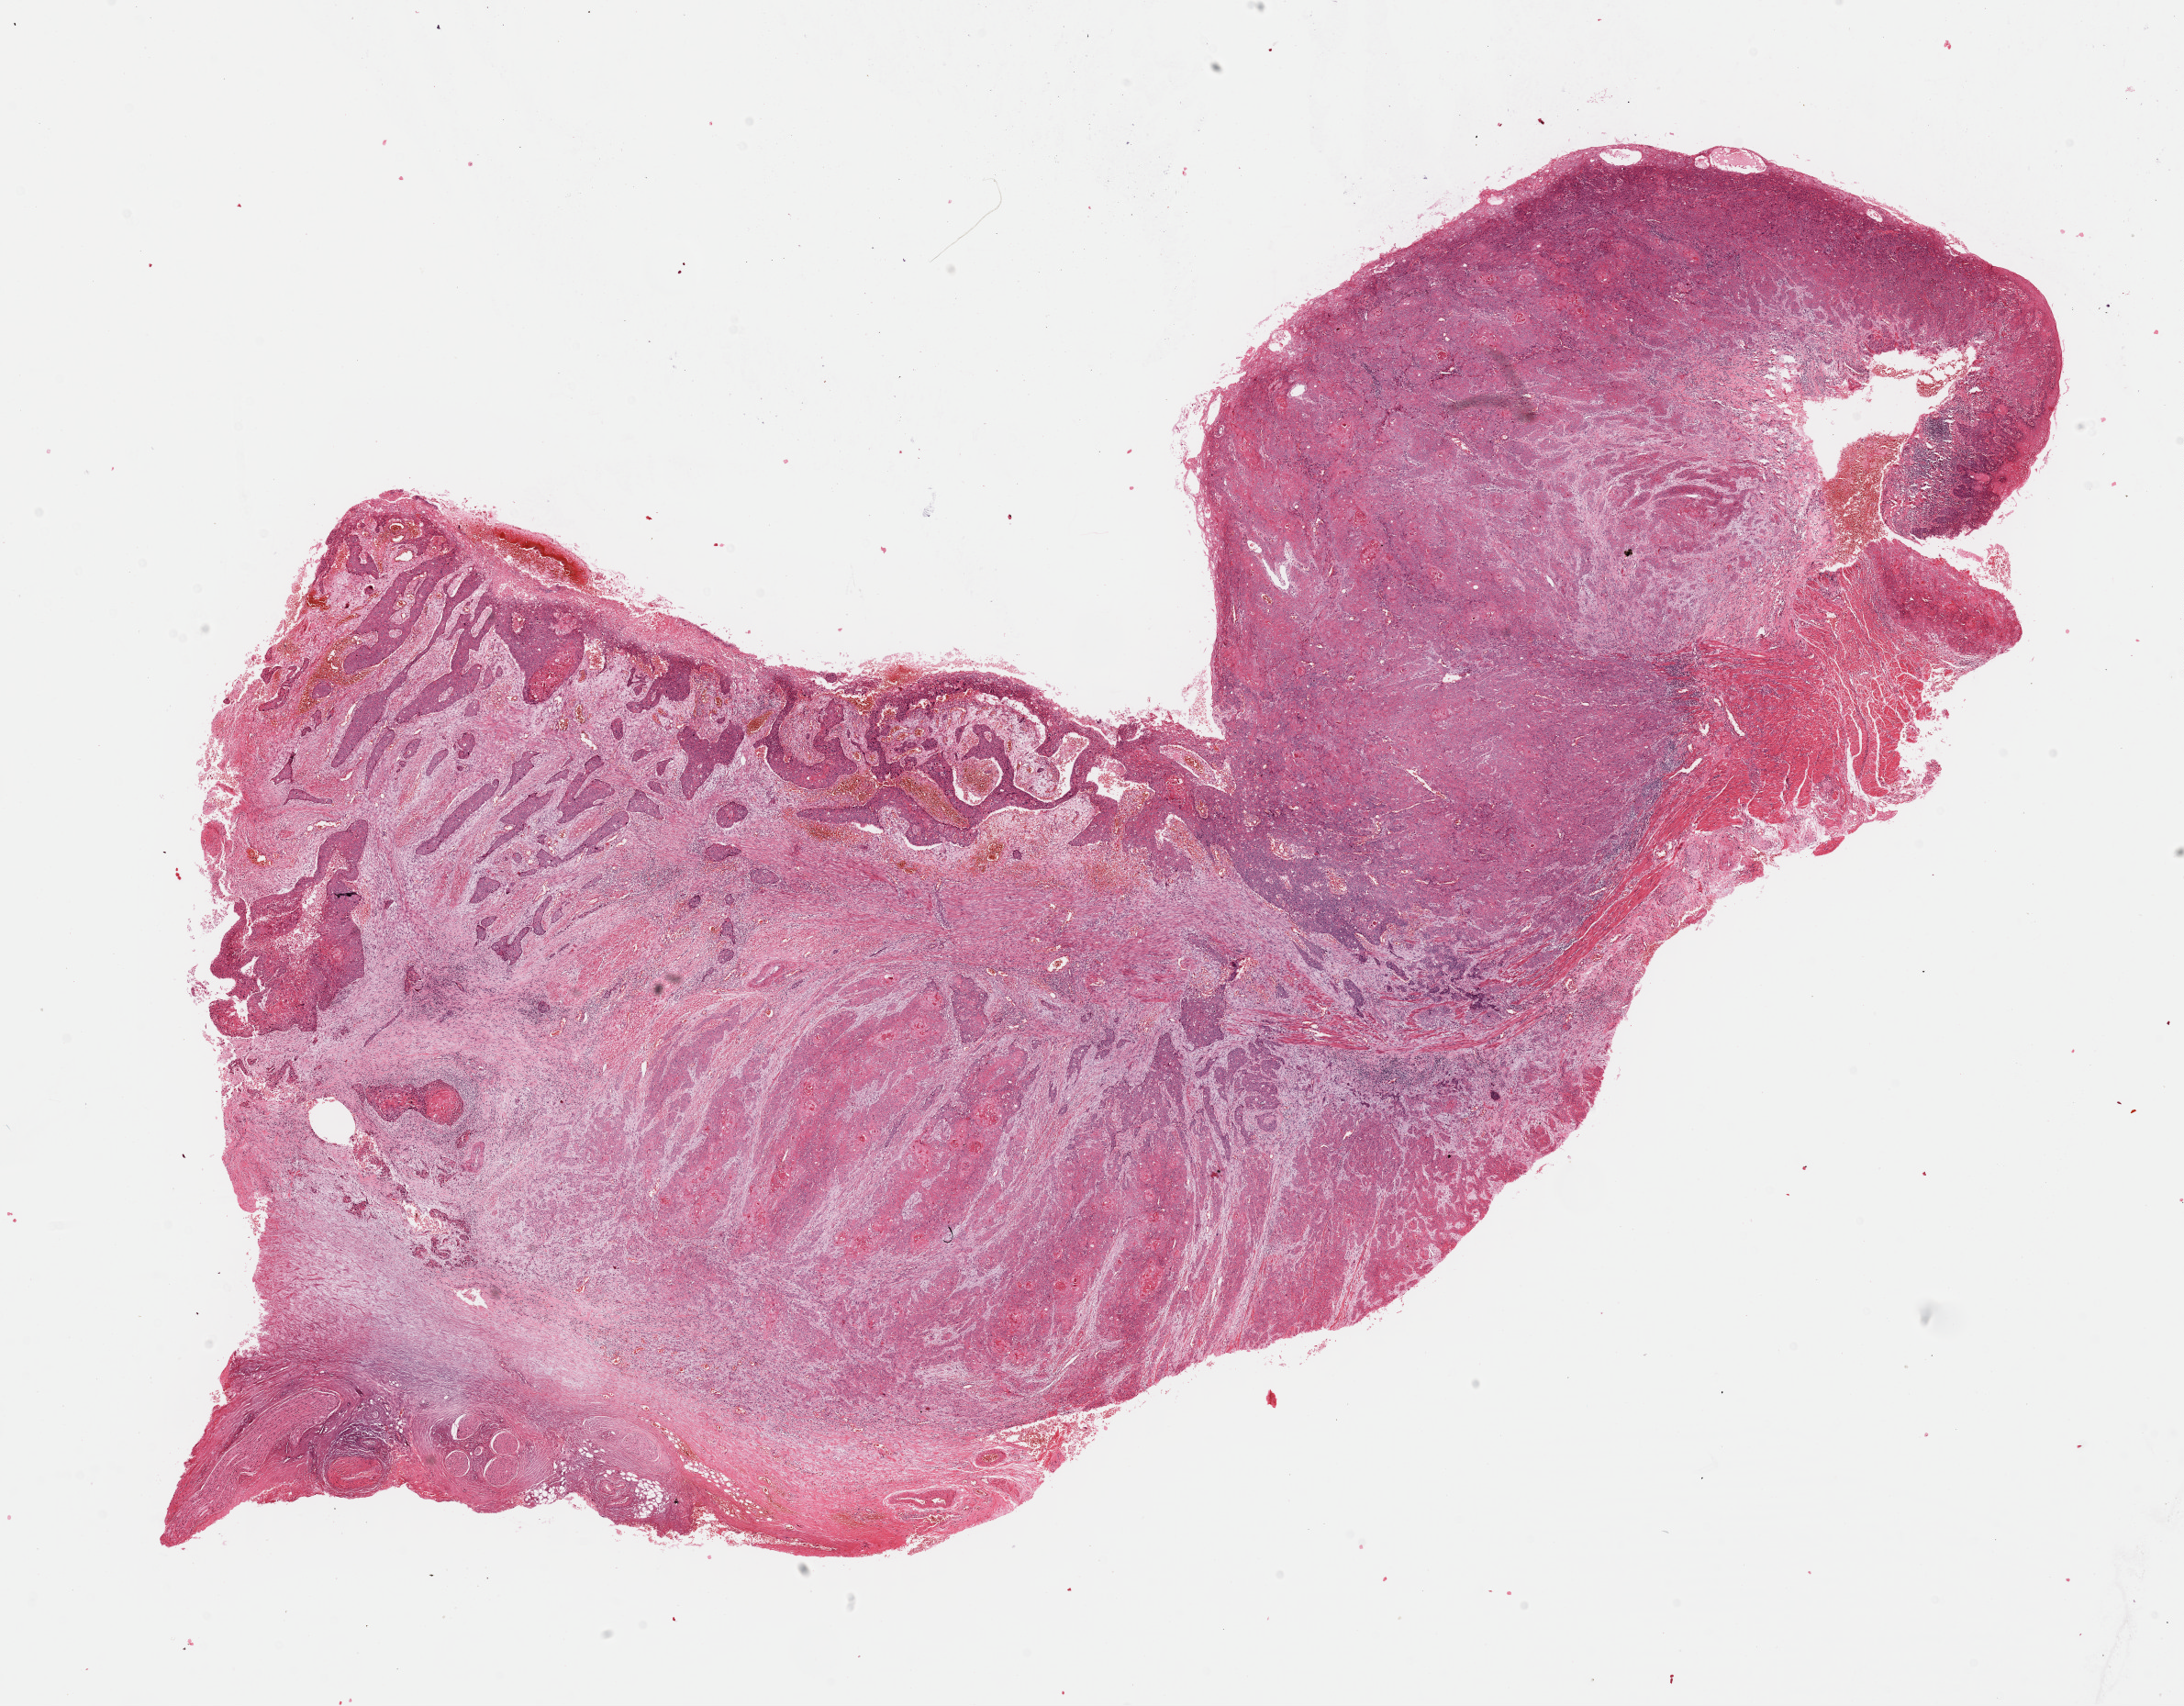
Hematoxylin and eosin (H&E) stained whole-slide image — shown as a low-resolution overview of the whole scanned area (about 18.8 x 14.7 mm), FFPE section, esophagus, primary tumour sample. Patient: male, age at initial diagnosis 58 years. Histologic grade: G1 (well differentiated).
Histologic diagnosis: Squamous cell carcinoma, NOS (middle third of esophagus). AJCC pathologic stage: IIA.